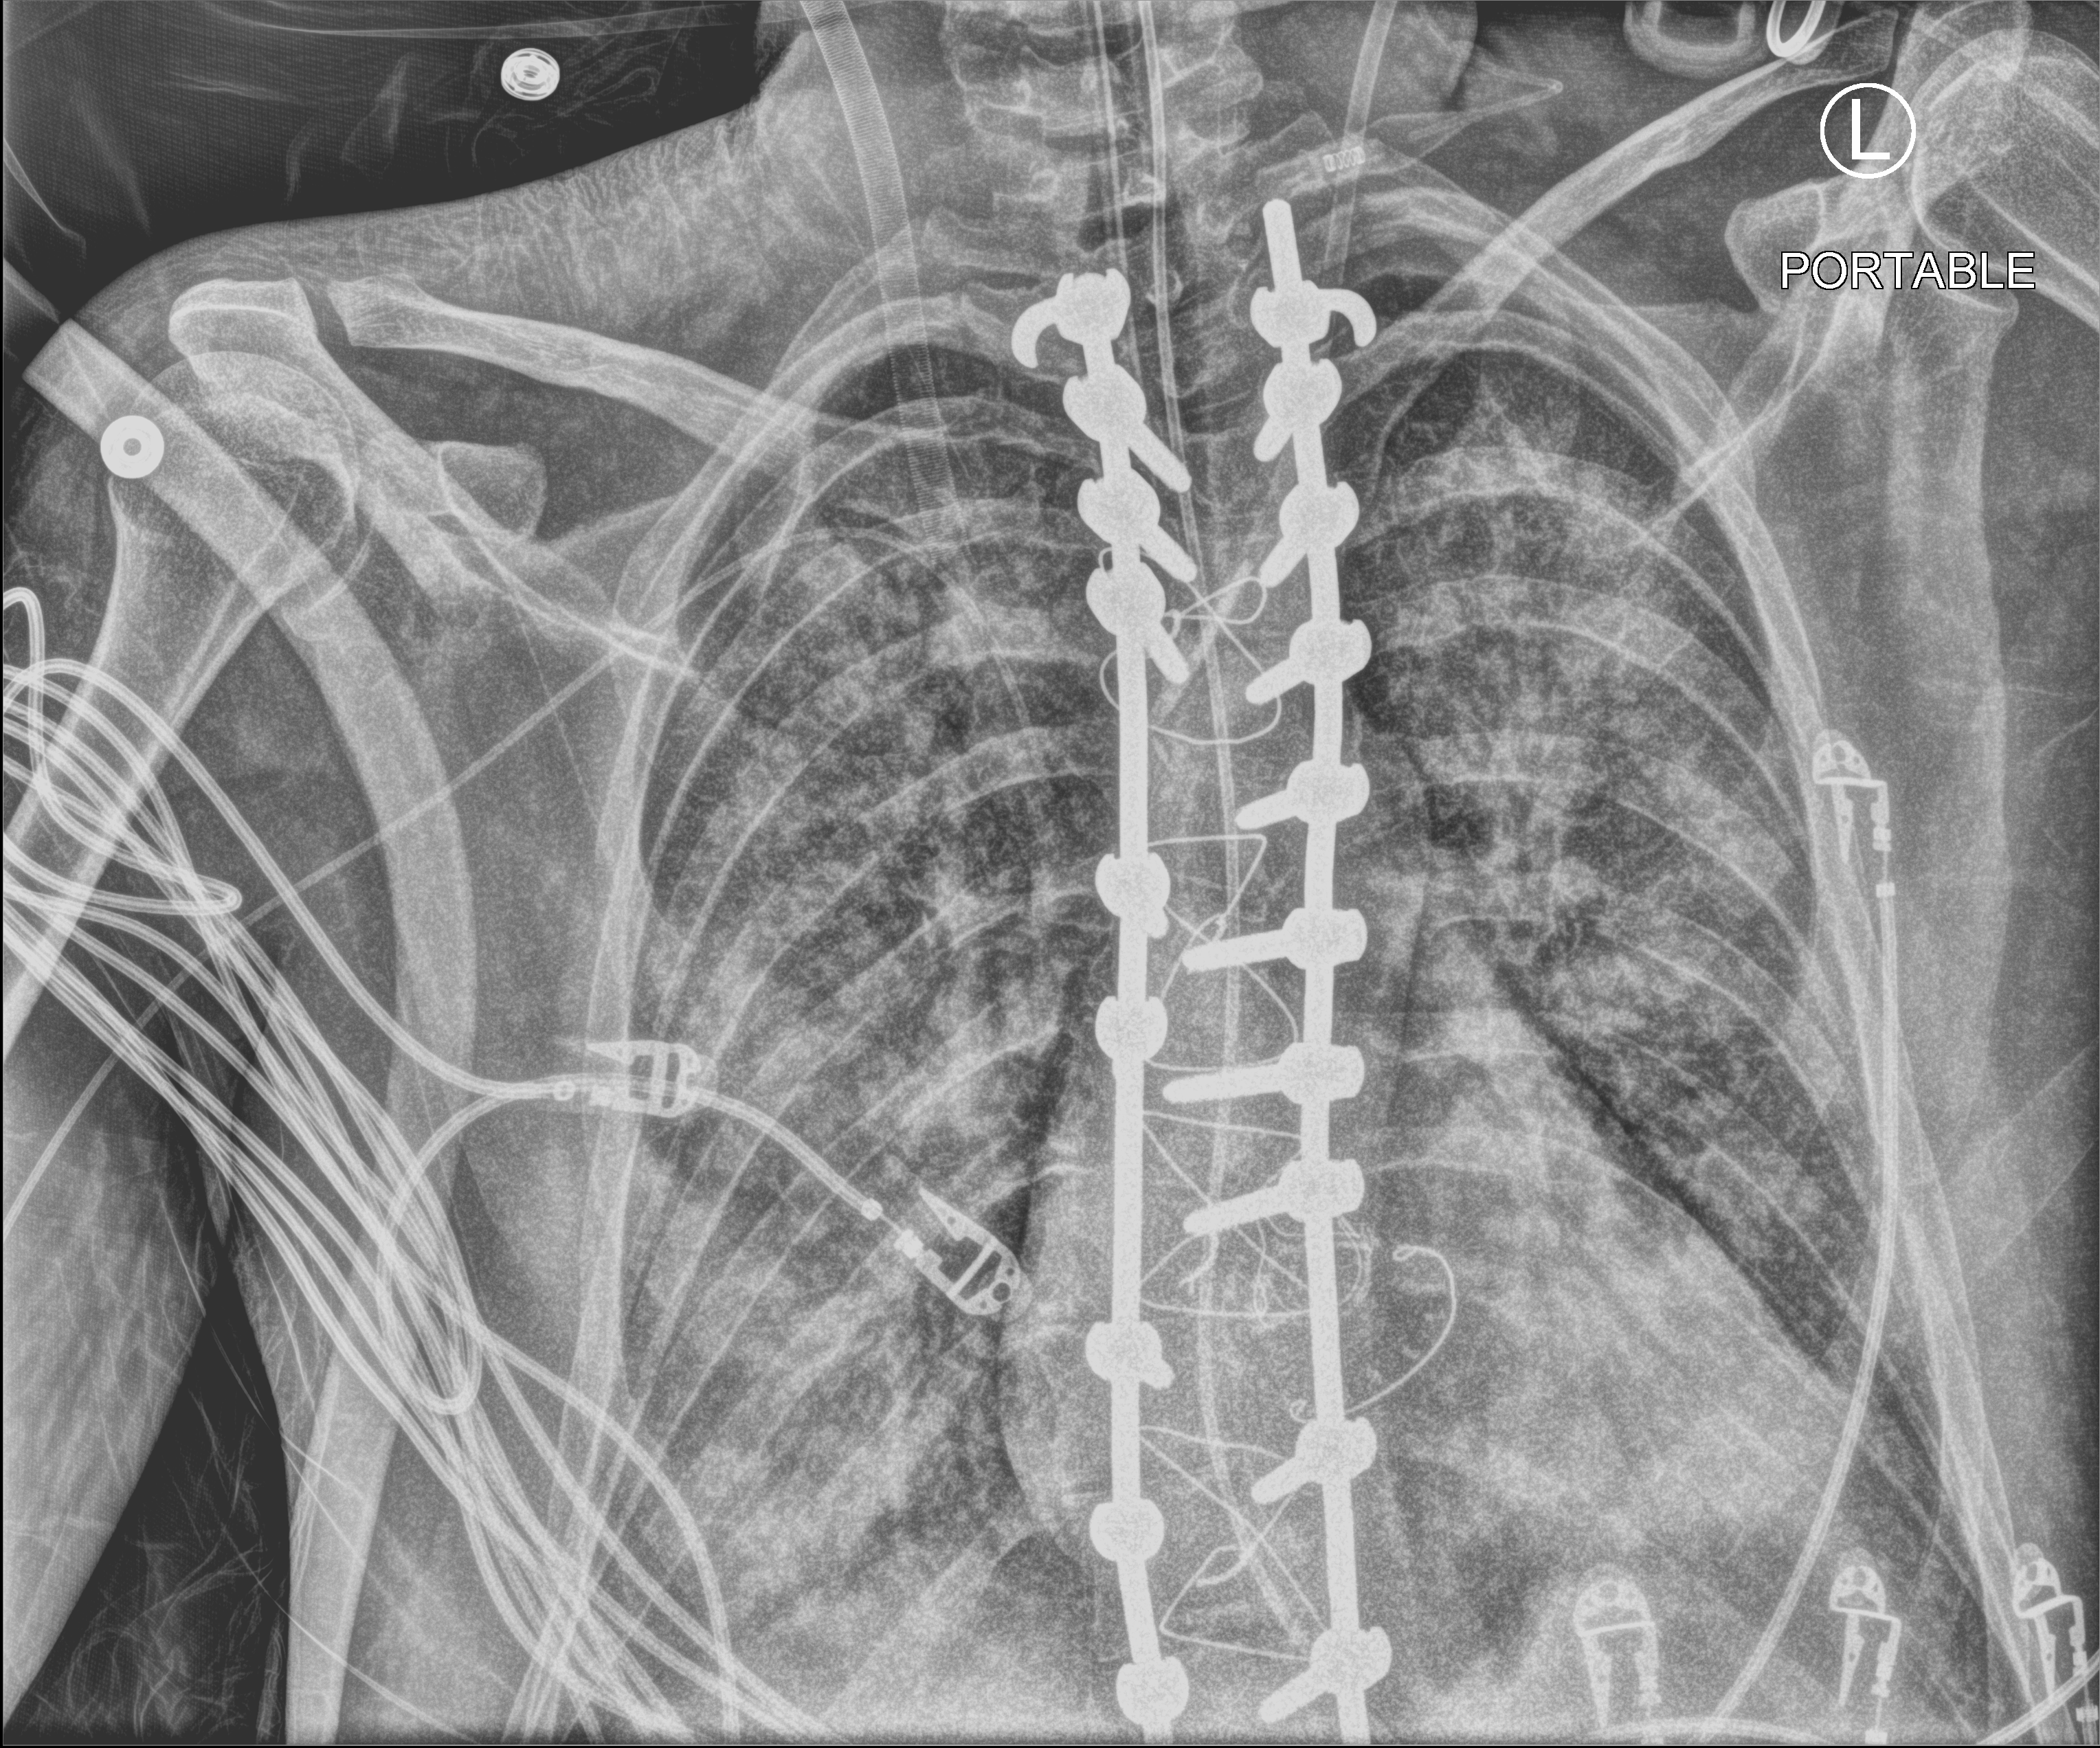
Chest X-ray (portable). Patient hospitalised with COVID-19, aged 18–59 years.
Hospital-stay facts (about this admission, not read from this image; timing relative to this image not recorded): mechanically ventilated during this hospital stay: yes; admitted to intensive care during this hospital stay: yes.